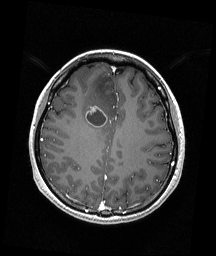
Brain MRI from a brain-tumour surgery series, one axial slice; position 65 of 192 along the scan axis; T1-weighted post-contrast; 1 mm slice thickness; 216 × 256 image matrix, field of view 211 × 250 mm. From the clinical record (not read from this slice): histopathology: Astrocytoma; WHO grade: 4; IDH mutation: yes; tumour location: Right Frontal.
Structures marked on this image (expert manual segmentation):
- tumour: bounding box (x1, y1, x2, y2) in pixels: (86, 106, 107, 127)